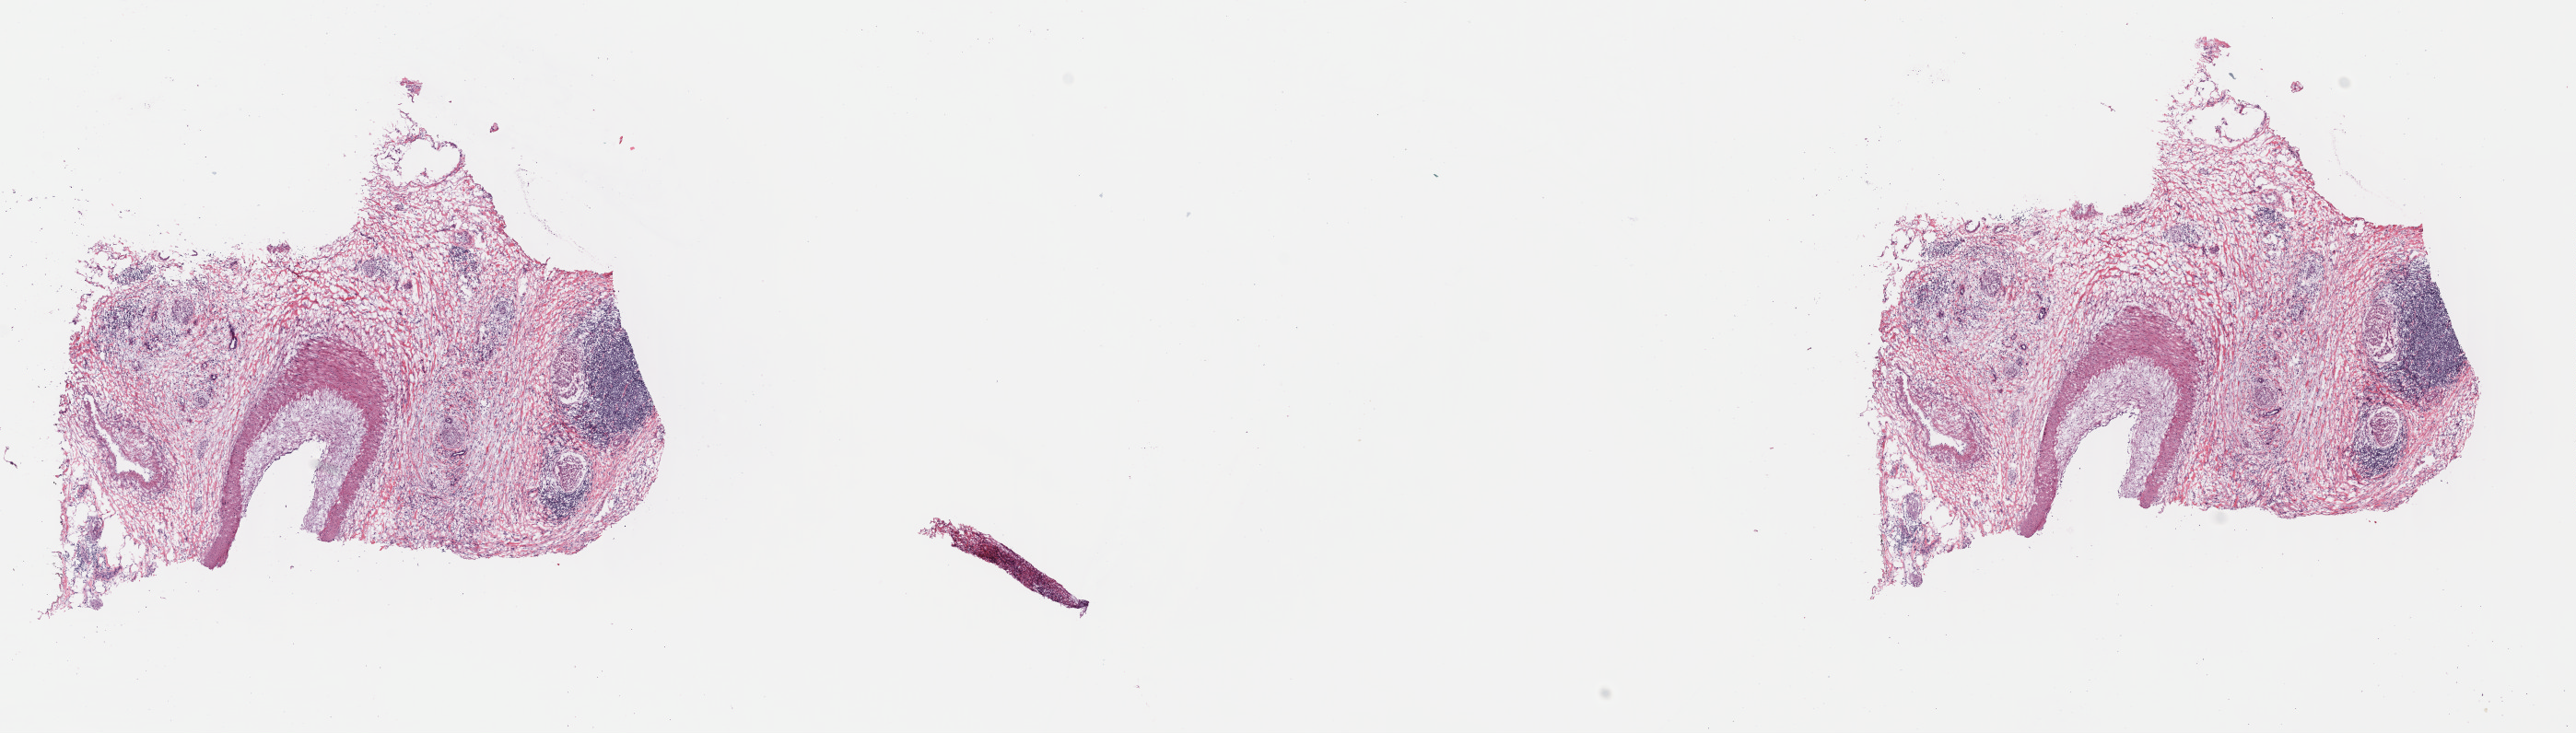
Whole-slide histology image, H&E-stained — a low-resolution overview of the entire scanned area, about 22.0 x 6.3 mm. Frozen section from the top of the tissue portion. Primary tumour sample from the pancreas. Female patient; age at initial diagnosis 55 years. Histologic grade: G2 (moderately differentiated). Pathologist review of this section (percent, as recorded): tumour cells 3%, tumour nuclei 3%, normal cells 97%, stromal cells 0%, necrosis 0%. Infiltration values recorded for this section: lymphocyte infiltration 8%, monocyte infiltration 0%, neutrophil infiltration 0%.
* AJCC pathologic stage: IIB (7th edition)
* lymph nodes positive (case pathology): 1 of 19 examined
* pathologic diagnosis: Adenocarcinoma, NOS